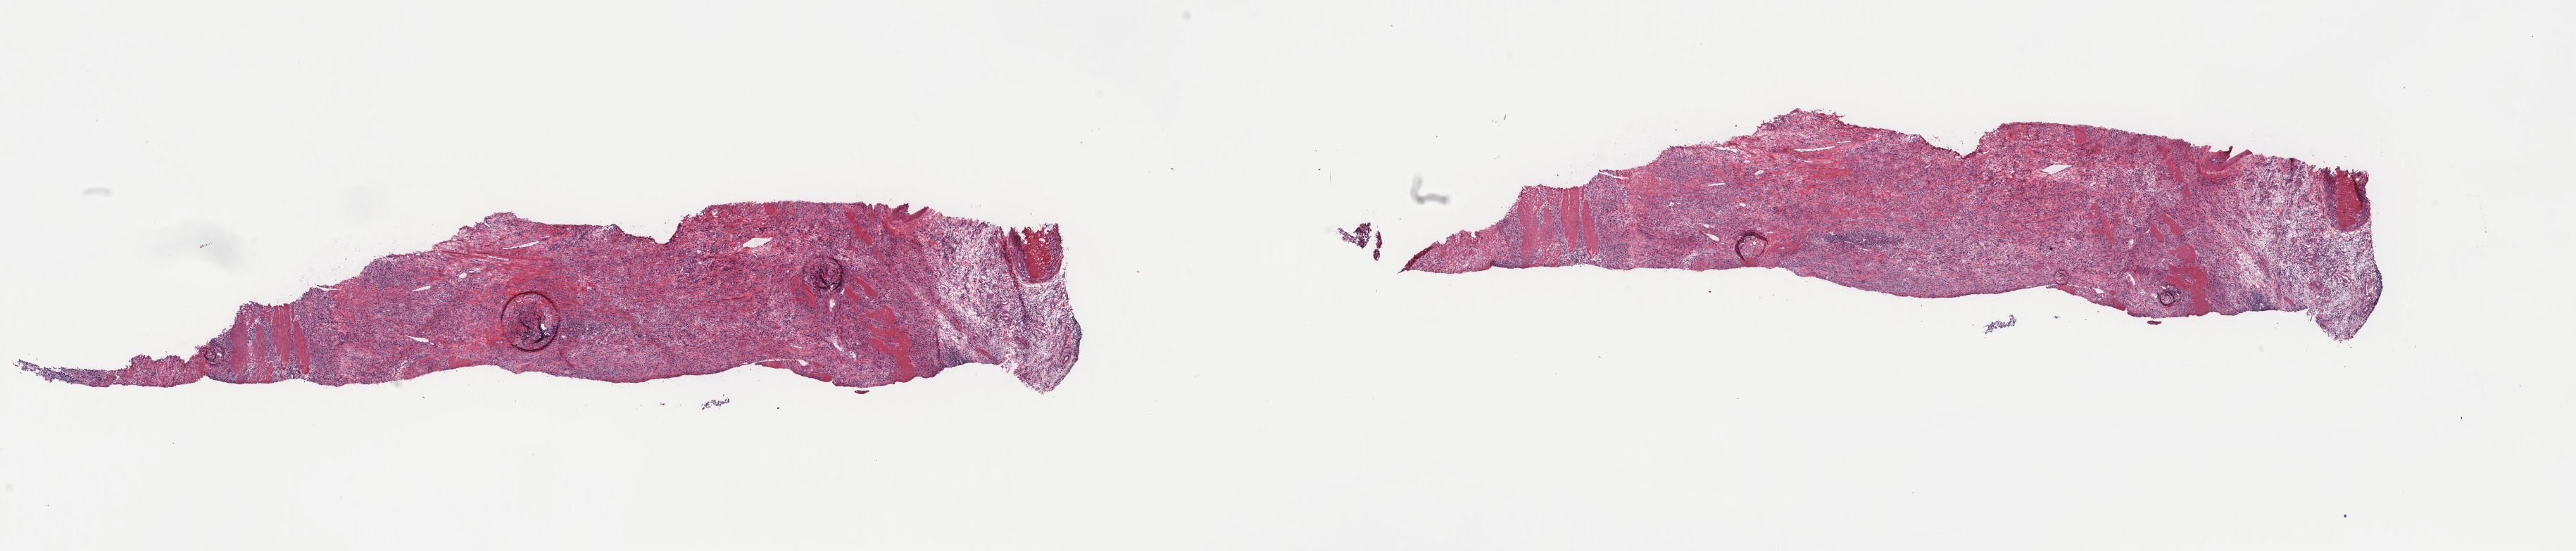
Digitized H&E-stained tissue section (whole slide), whole scanned area (about 29.0 x 6.2 mm, from a 40x scan) shown as a low-resolution overview. Frozen section from the top of the tissue portion. Sample: primary tumour, stomach. Female patient; age at initial diagnosis 34 years. Histologic grade: G3 (poorly differentiated). Composition of this section per pathologist review: tumour cells 60%, tumour nuclei 80%, normal cells 0%, stromal cells 40%, necrosis 0%. Infiltration values recorded for this section: lymphocyte infiltration 0%, monocyte infiltration 0%, neutrophil infiltration 0%.
TNM: T4a N1 M0. AJCC pathologic stage: IIIA (7th edition). Diagnosis: Adenocarcinoma, NOS. Lymph nodes positive (case pathology): 1 of 6 examined.